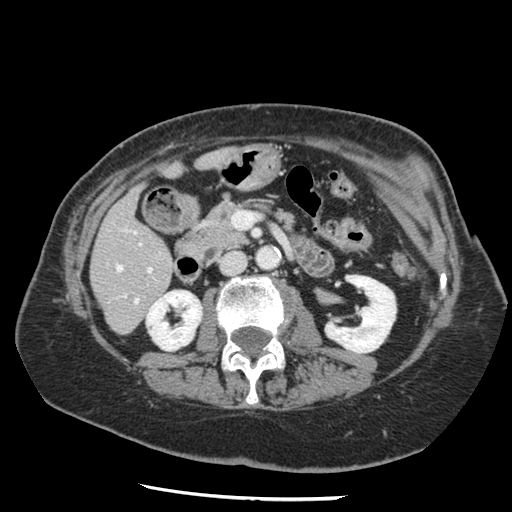
Contrast-enhanced abdominal CT, one axial slice; position 52 of 148 along the scan axis; 120 kVp; soft-tissue window (W 400 / L 40 HU); 512 × 512 image matrix, field of view 330 × 330 mm. Female patient, age 85 years. Case-level facts recorded for this patient, not image findings: diagnosis: colorectal cancer liver metastases, imaged before liver resection.
Structures marked on this image (manually delineated by an expert):
- hepatic veins: bounding box (x1, y1, x2, y2) in pixels: (116, 265, 138, 303)
- liver: (92, 150, 228, 333)
- planned liver remnant (the part of the liver to remain after resection): (92, 150, 228, 329)